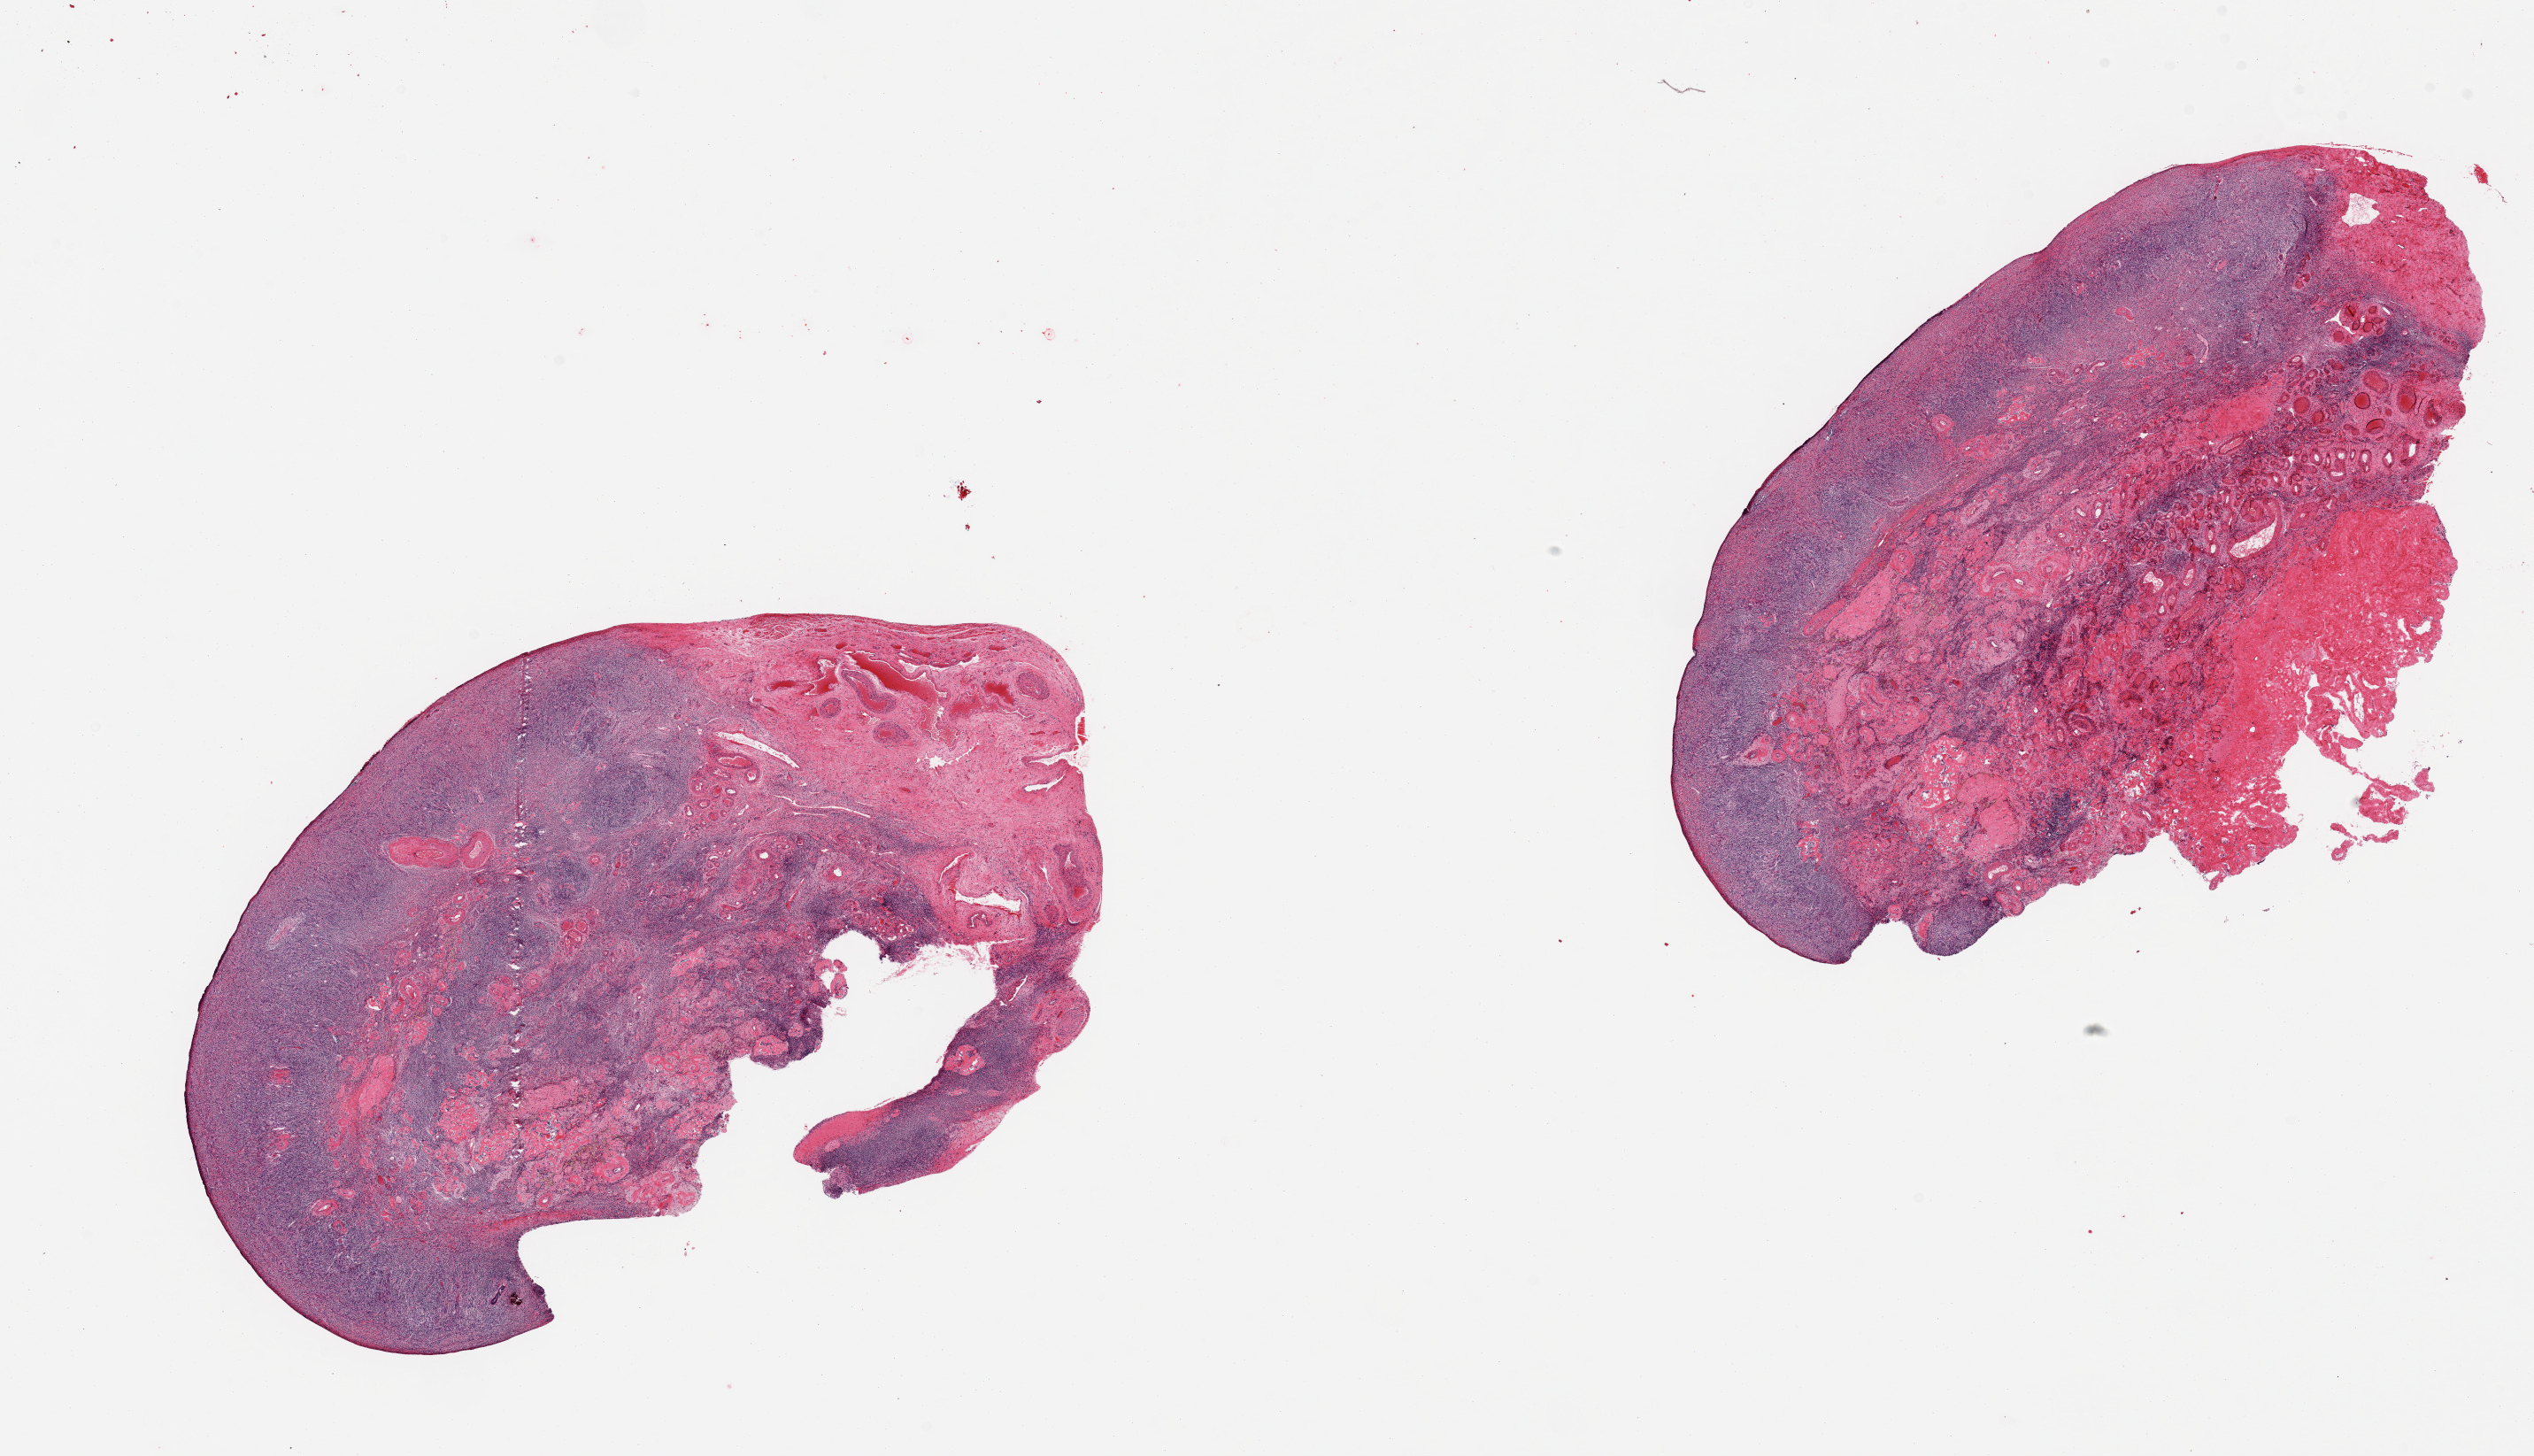
Digitized haematoxylin and eosin-stained section — shown as a low-resolution overview of the whole scanned area (about 22.6 x 13.0 mm), PAXgene-fixed paraffin-embedded (PFPE) section, target tissue: ovary, tissue donor sample. Donor sex: female.
Review note (as recorded): 2 pieces; atrophic.